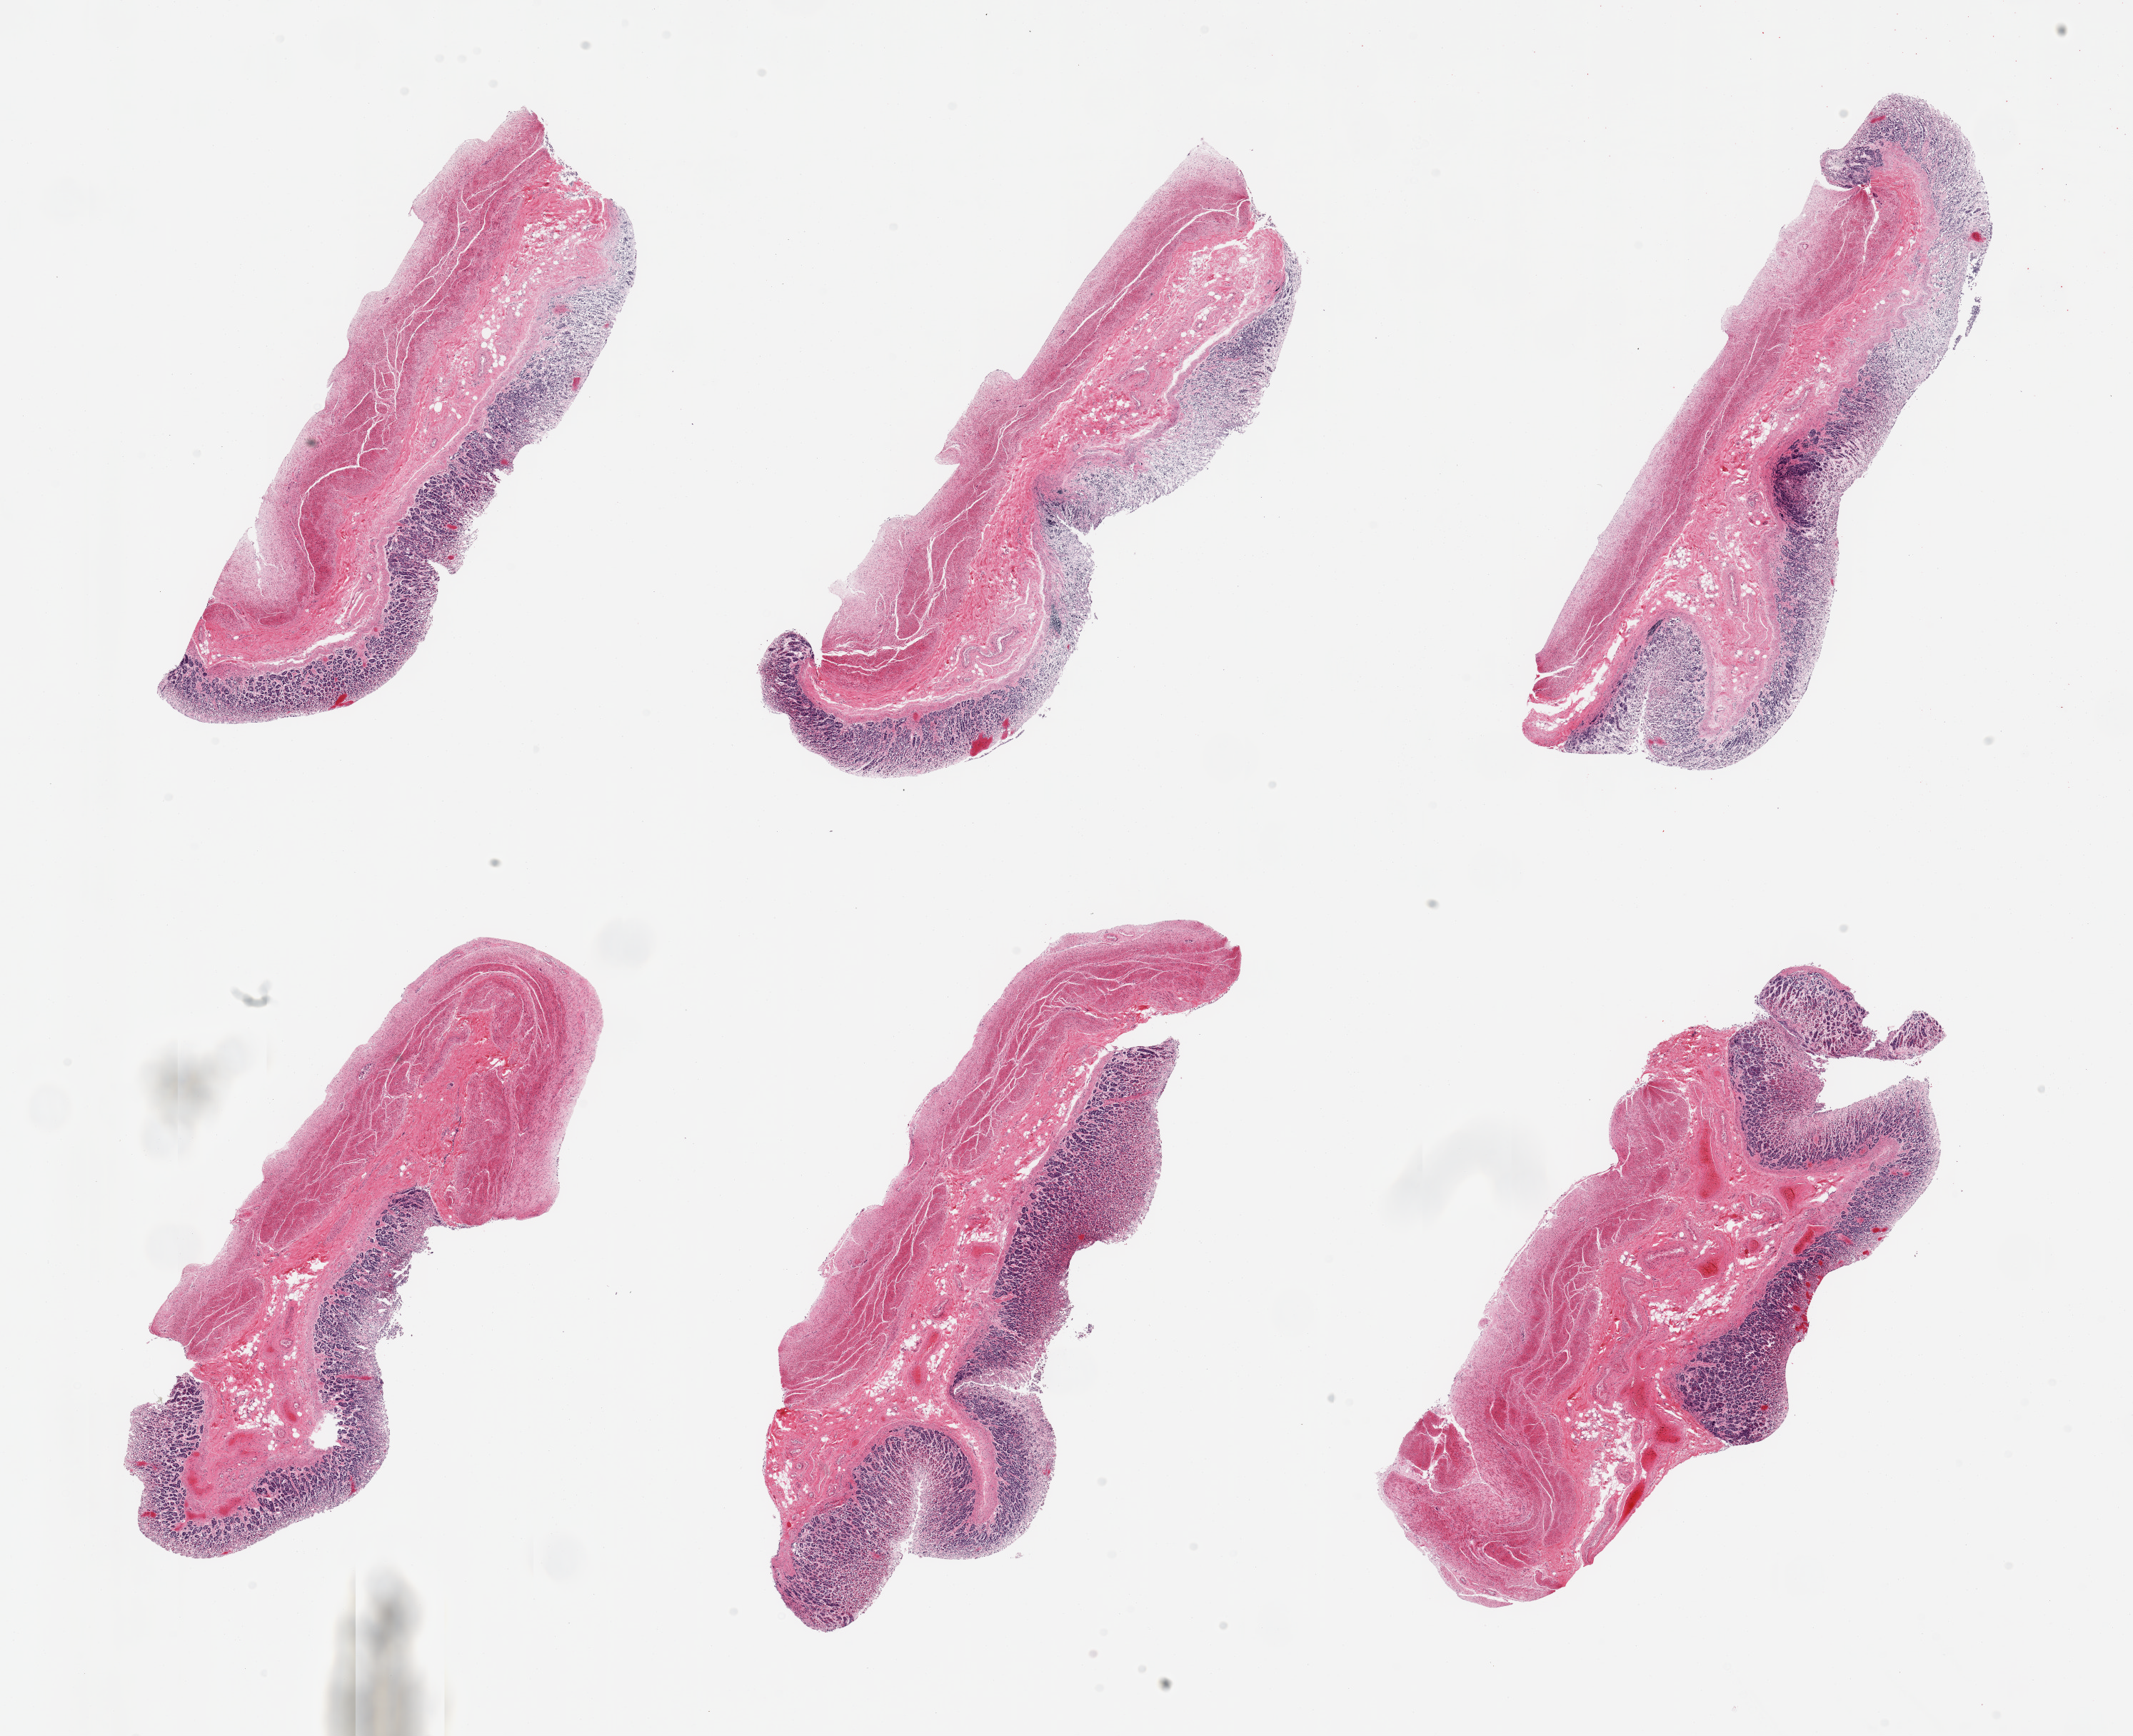
H&E whole-slide image, a low-resolution overview of the entire scanned area, about 23.6 x 19.2 mm (slide scanned at 20x), PAXgene-fixed paraffin-embedded (PFPE) section, target tissue: stomach, donor tissue sample.
Pathologist's review note for this sample: 6 pieces mucosa is ~1mm, severely autolyzed.